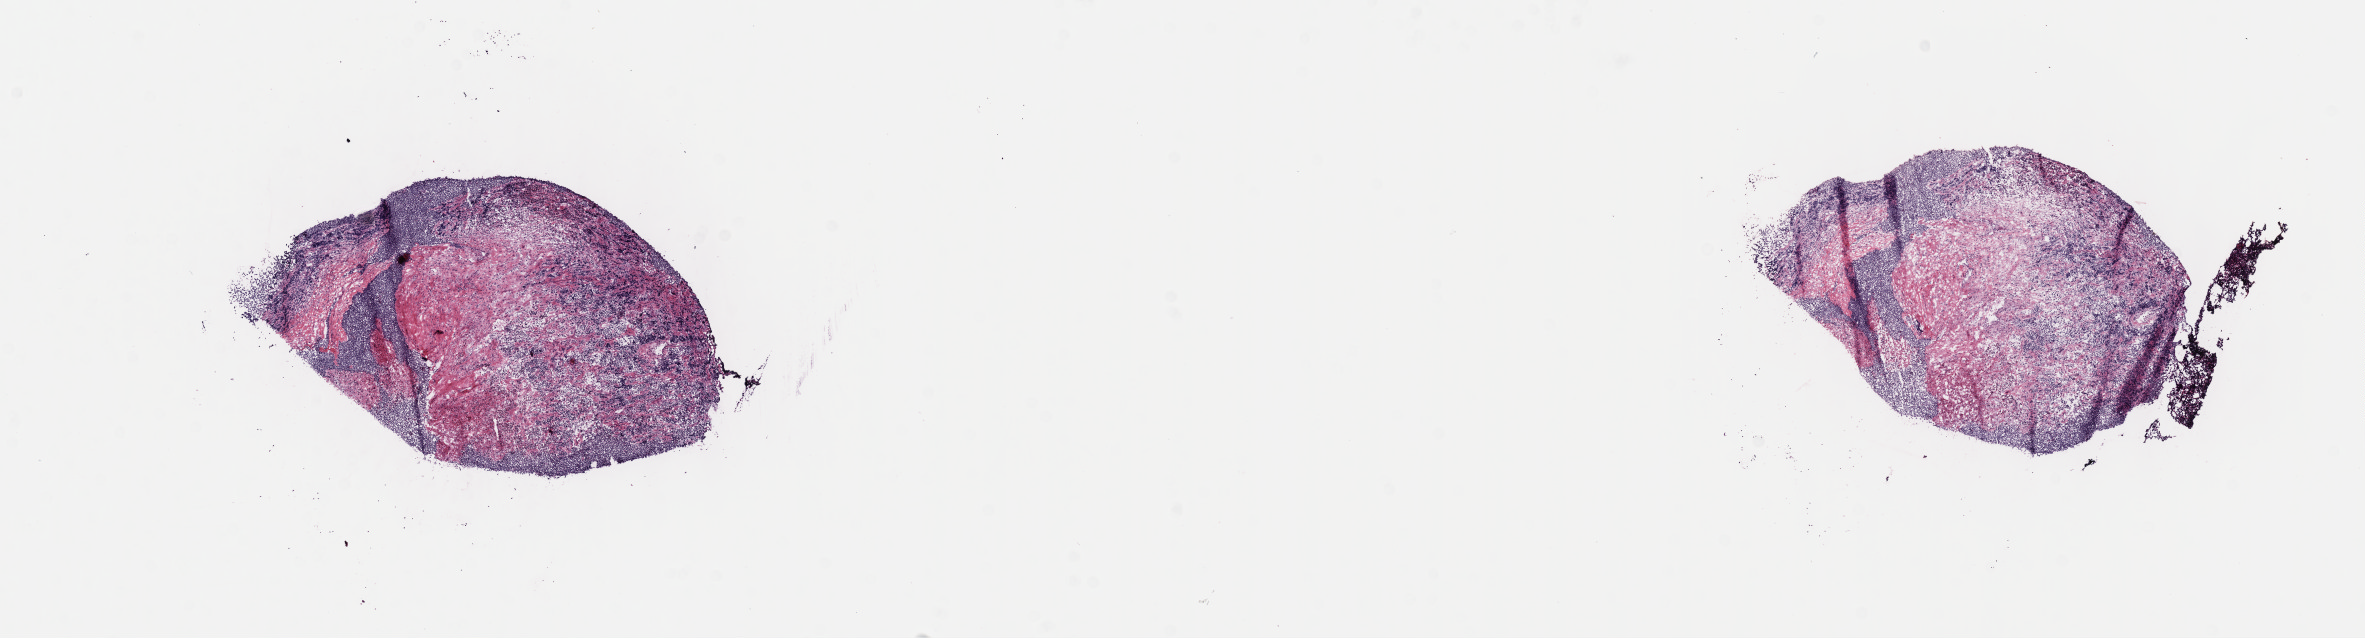
Hematoxylin and eosin (H&E) whole-slide image, low-resolution overview of the scanned area, about 19.1 x 5.2 mm, frozen section, primary tumor, site: cranium. Patient: male, age at initial diagnosis 6 years.
Diagnosis: Burkitt lymphoma, NOS.